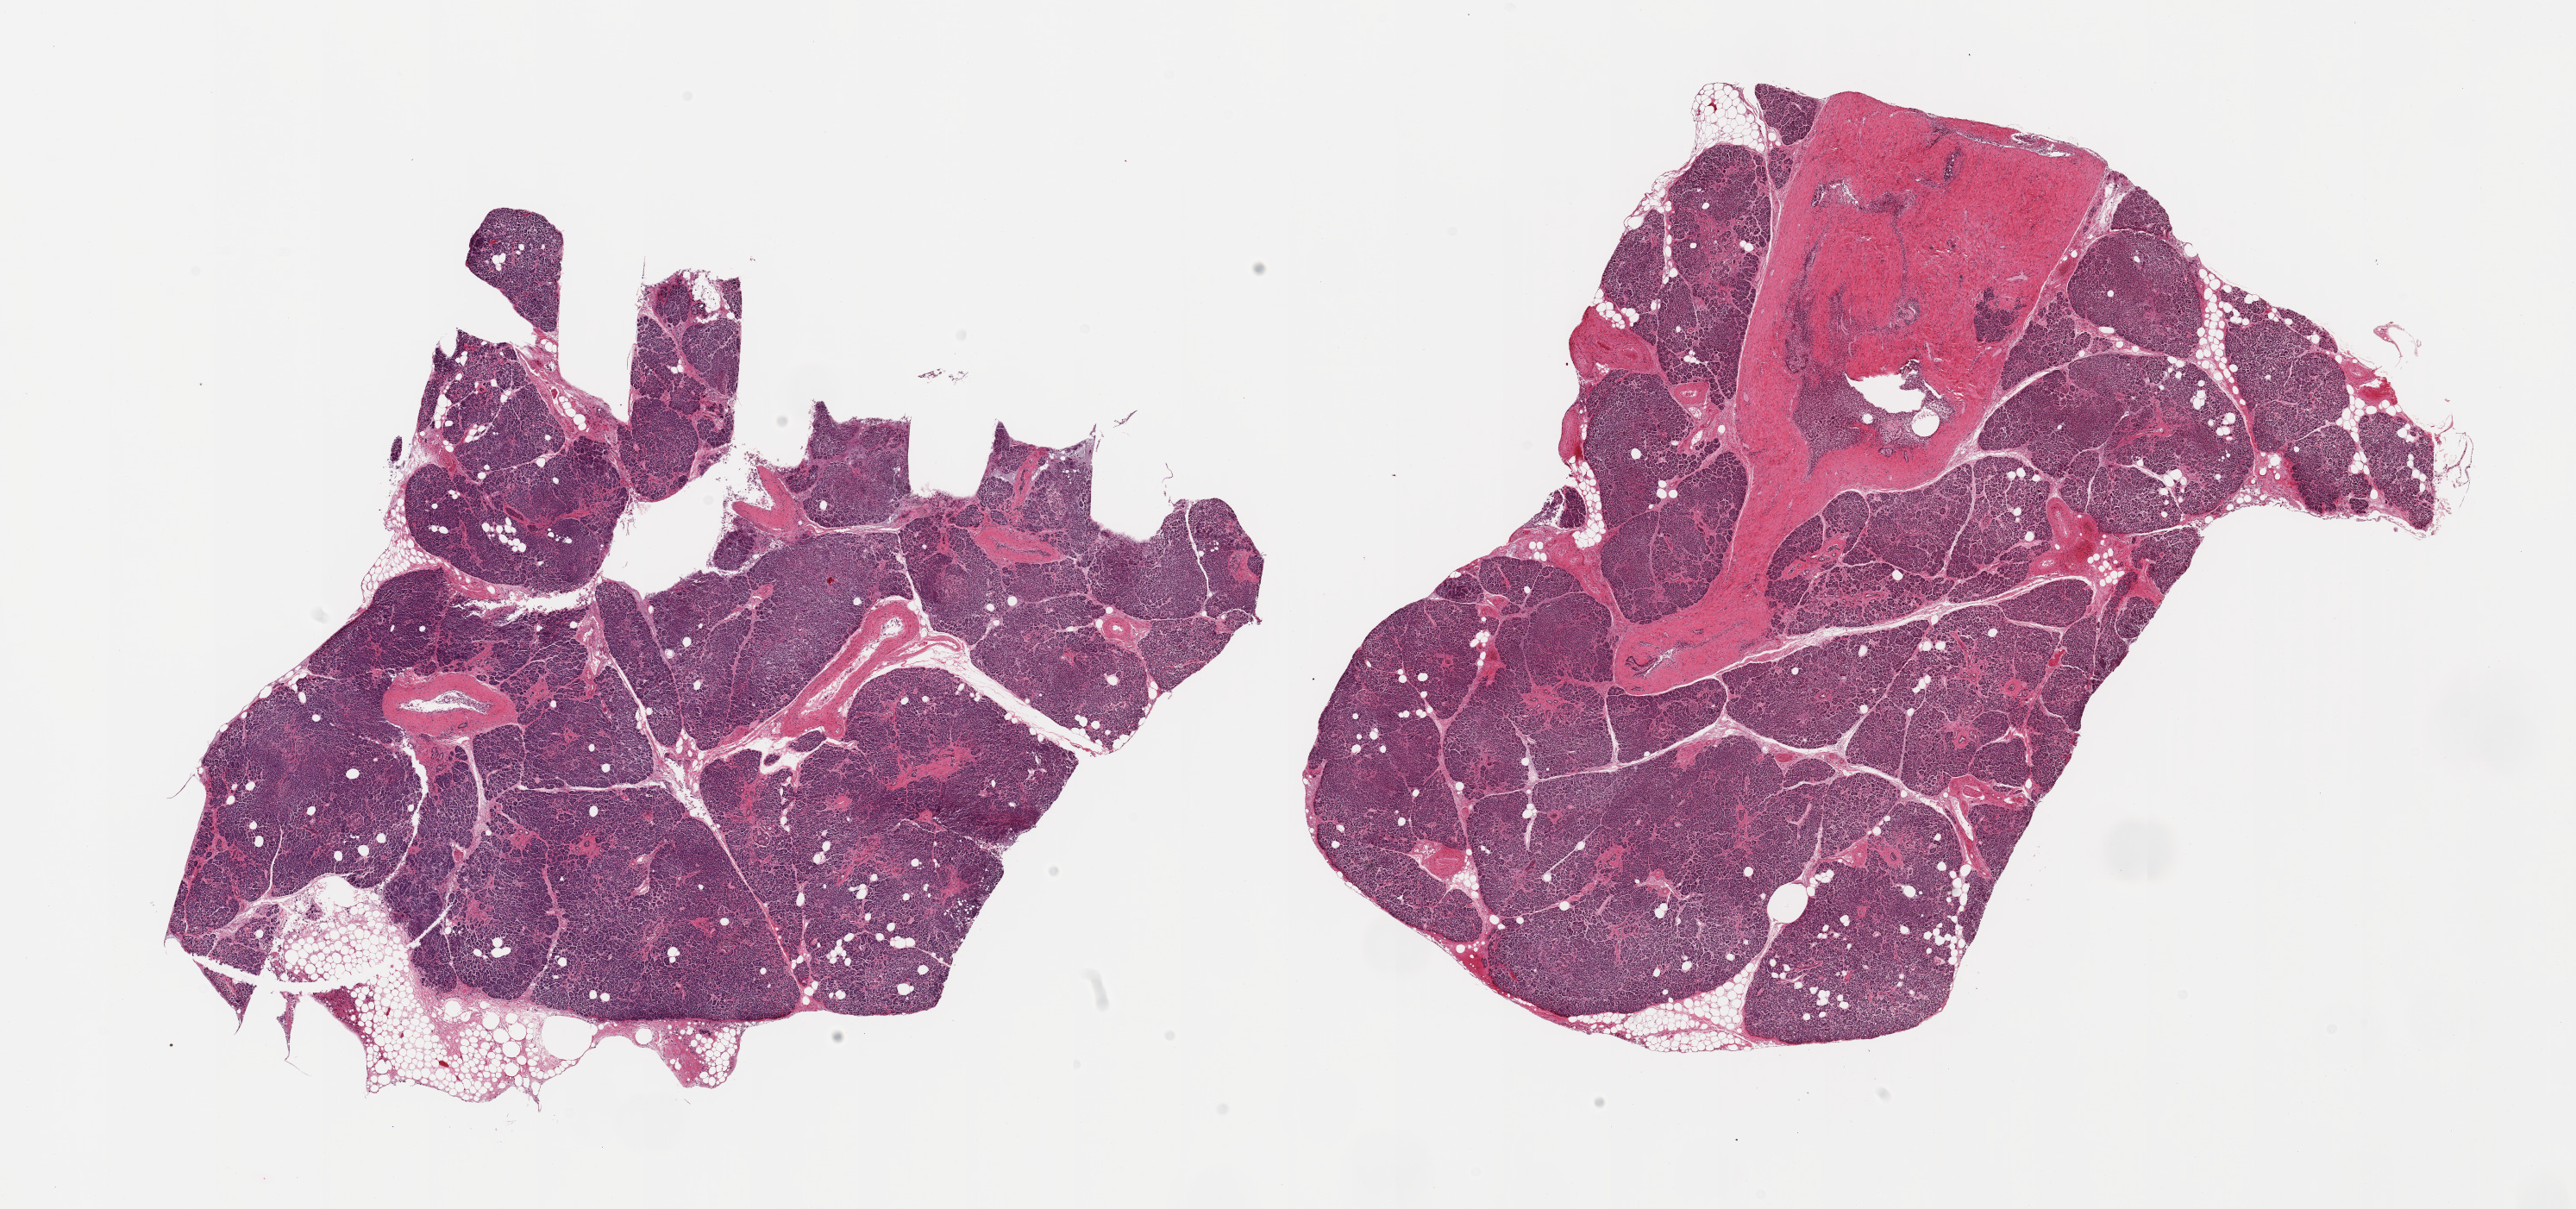
Whole-slide image, haematoxylin and eosin stain, whole scanned area (about 23.6 x 11.1 mm) shown as a low-resolution overview. PAXgene-fixed paraffin-embedded (PFPE) section. Sampled site (target tissue): pancreas. Donor tissue sample. Donor: female.
Reviewer comment on this tissue sample: 2 pieces, moderate-marked saponification, Islets poorly preserved; a rare one visible.